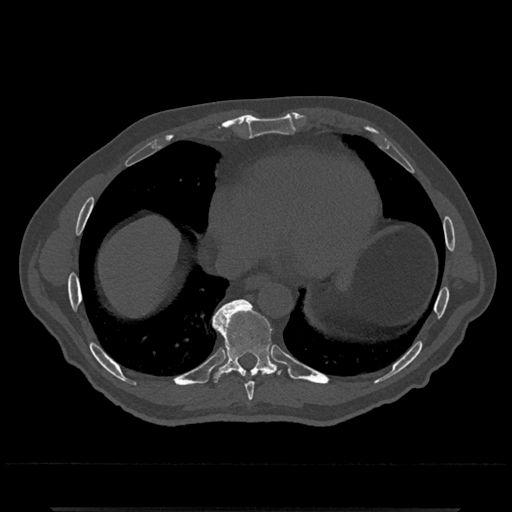
CT including the spine, one axial slice. Reconstruction kernel Br40s/3. 120 kVp. Bone window (W 1800 / L 400 HU). 512 × 512 image matrix, field of view 393 × 393 mm. Male patient, age 67 years. Case-level facts recorded for this patient, not image findings: primary cancer: prostate.
Structures marked on this image (semi-automatically segmented with operator editing):
- T8 vertebra: box from (x=245, y=382) to (x=254, y=401) px
- T9 vertebra: (x=212, y=300)–(x=285, y=385)